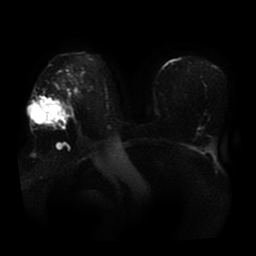
Breast MRI, one axial slice. Position 28 of 41 along the scan axis. Diffusion-weighted series; image 2 of 4 stored at this slice position (different b-values; order by instance number). 1.5 T. 5 mm slice thickness. 256 × 256 image matrix, field of view 360 × 360 mm. Female patient.
Annotated regions visible in this slice (outlined manually by an expert reader):
- tumour on diffusion-weighted imaging: bounding box [x1, y1, x2, y2] px = [31, 106, 60, 126]